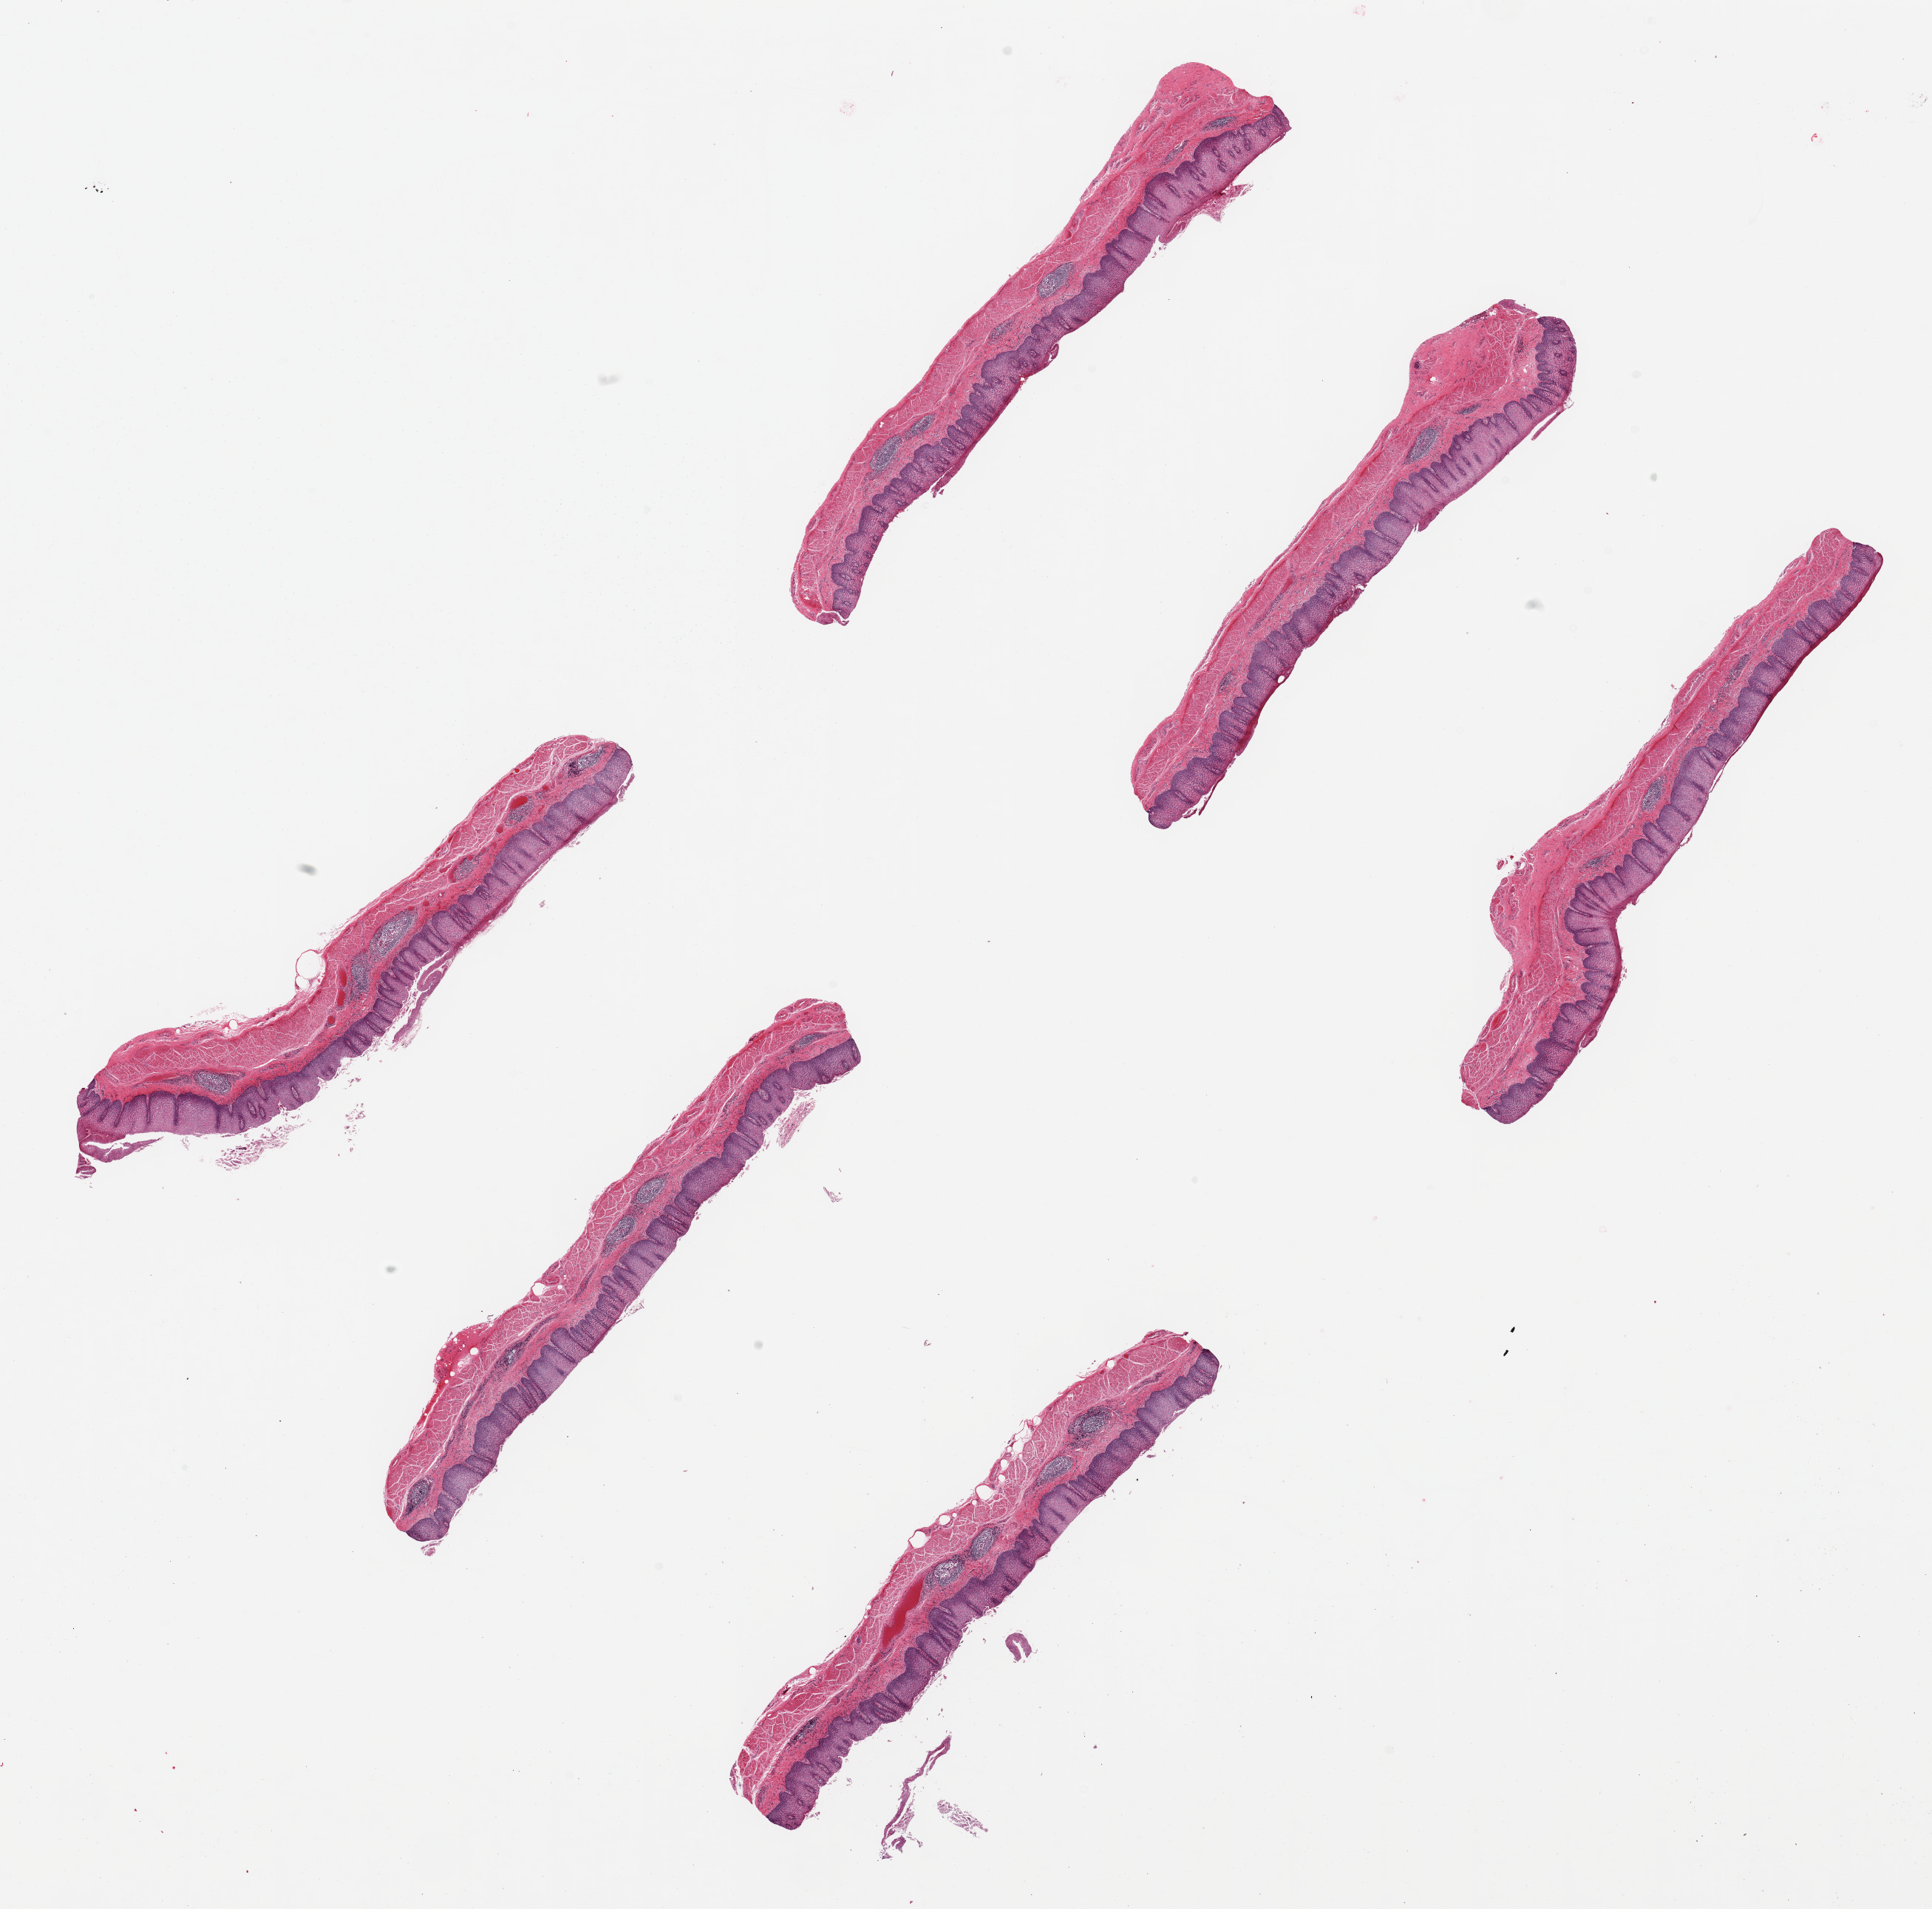
Whole-slide image, haematoxylin and eosin stain — low-resolution overview of the scanned area, about 20.7 x 20.4 mm (slide scanned at 20x), PAXgene-fixed paraffin-embedded (PFPE) section, target tissue: esophageal mucous membrane, donor tissue sample. Donor sex: female.
Reviewer comment on this tissue sample: 6 ~7x1mm pieces. Squamous mucosa focally sloughing, ~ 40-50% of thickness.